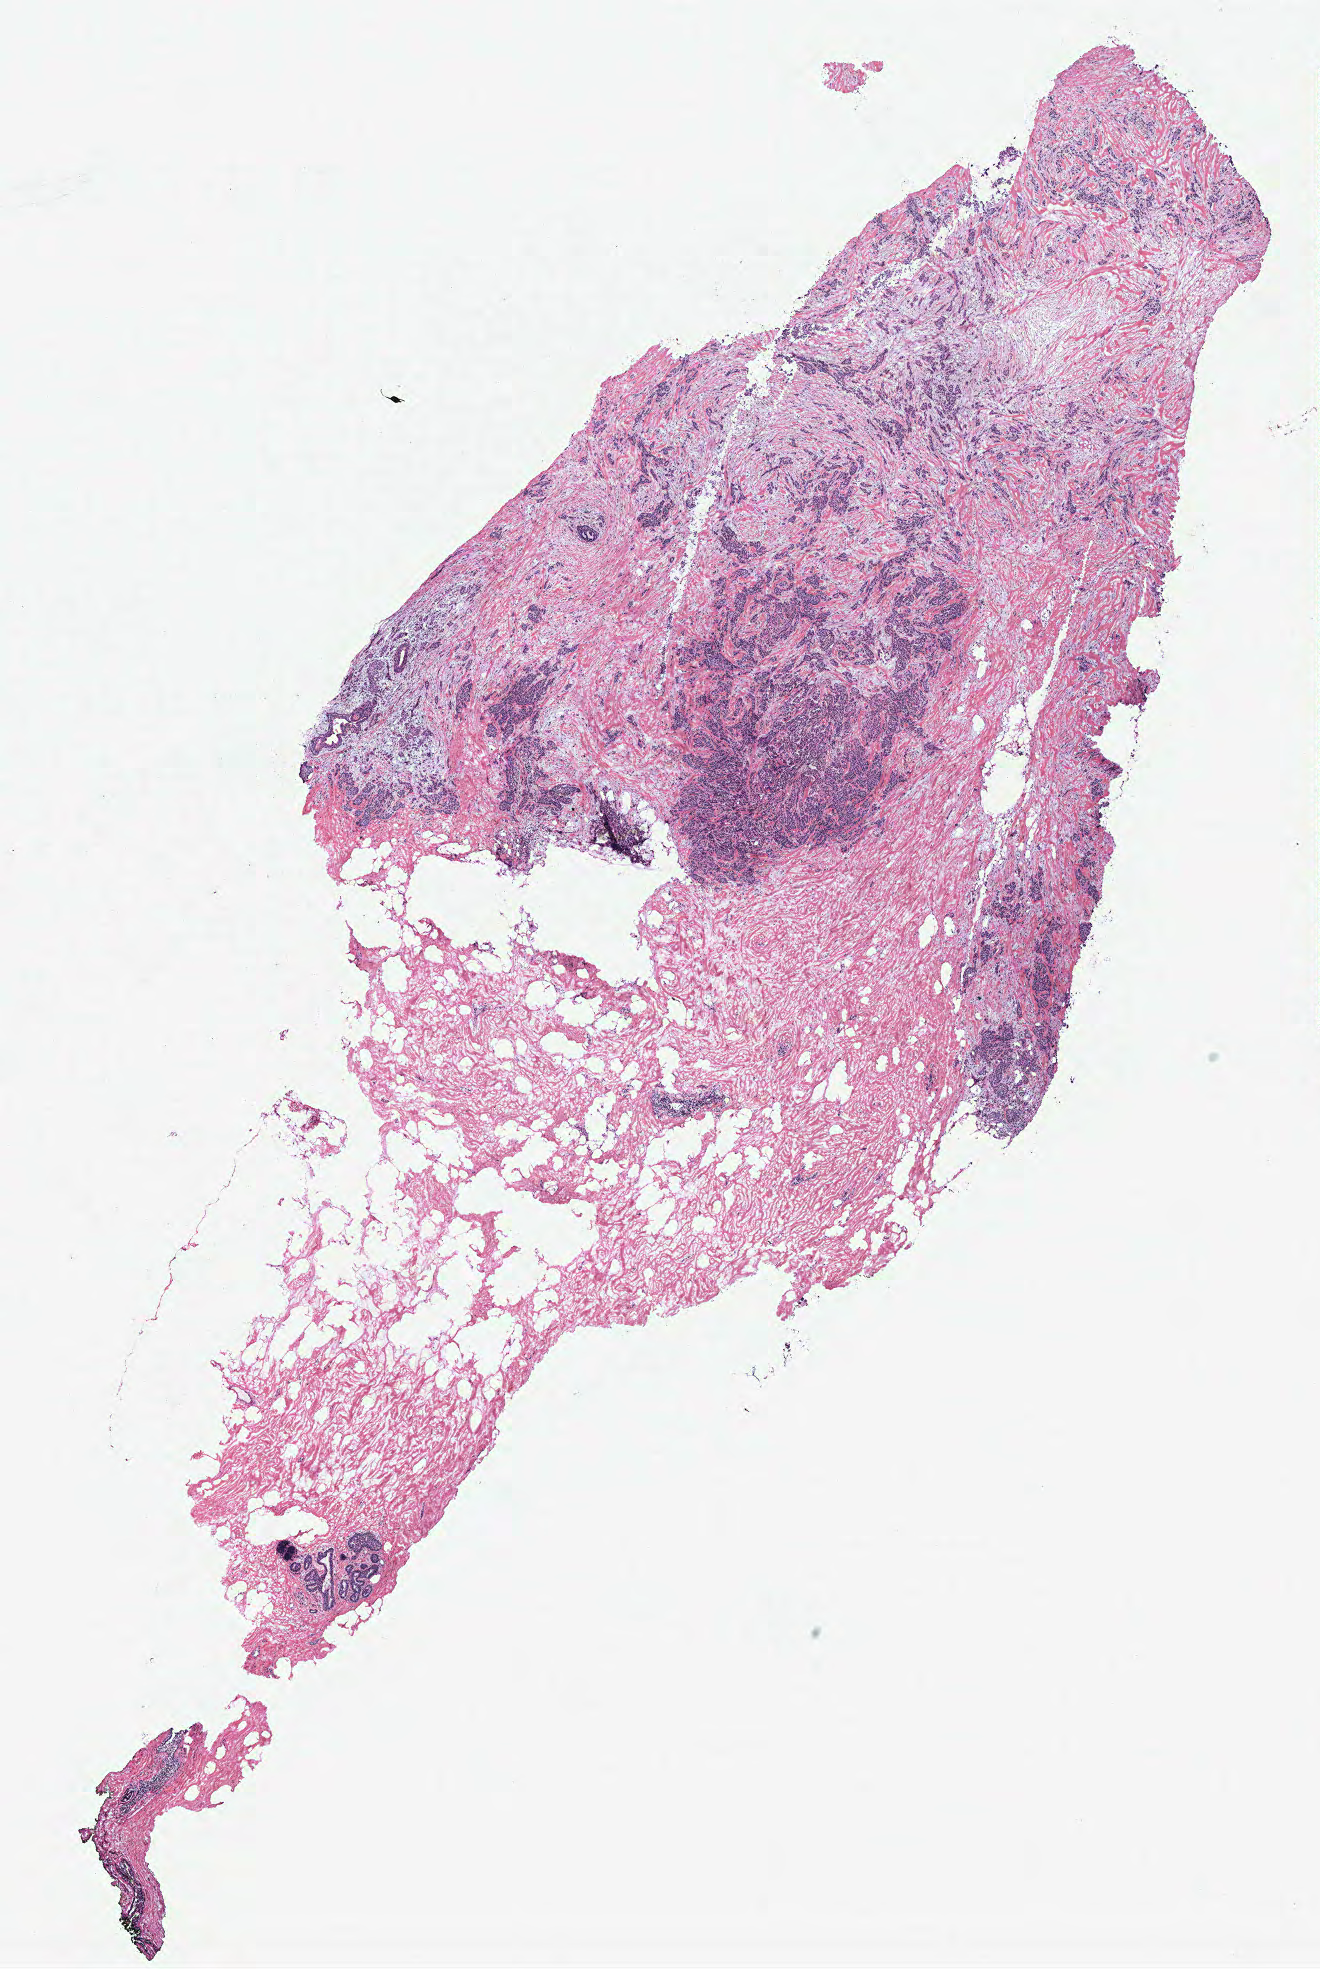
Digitized H&E tissue section (whole slide), shown as a low-resolution overview of the whole scanned area (about 10.6 x 15.8 mm, from a 40x scan), breast, tissue type not recorded. Patient: female, age 52 years.
Patient diagnosis: Infiltrating duct carcinoma, NOS.